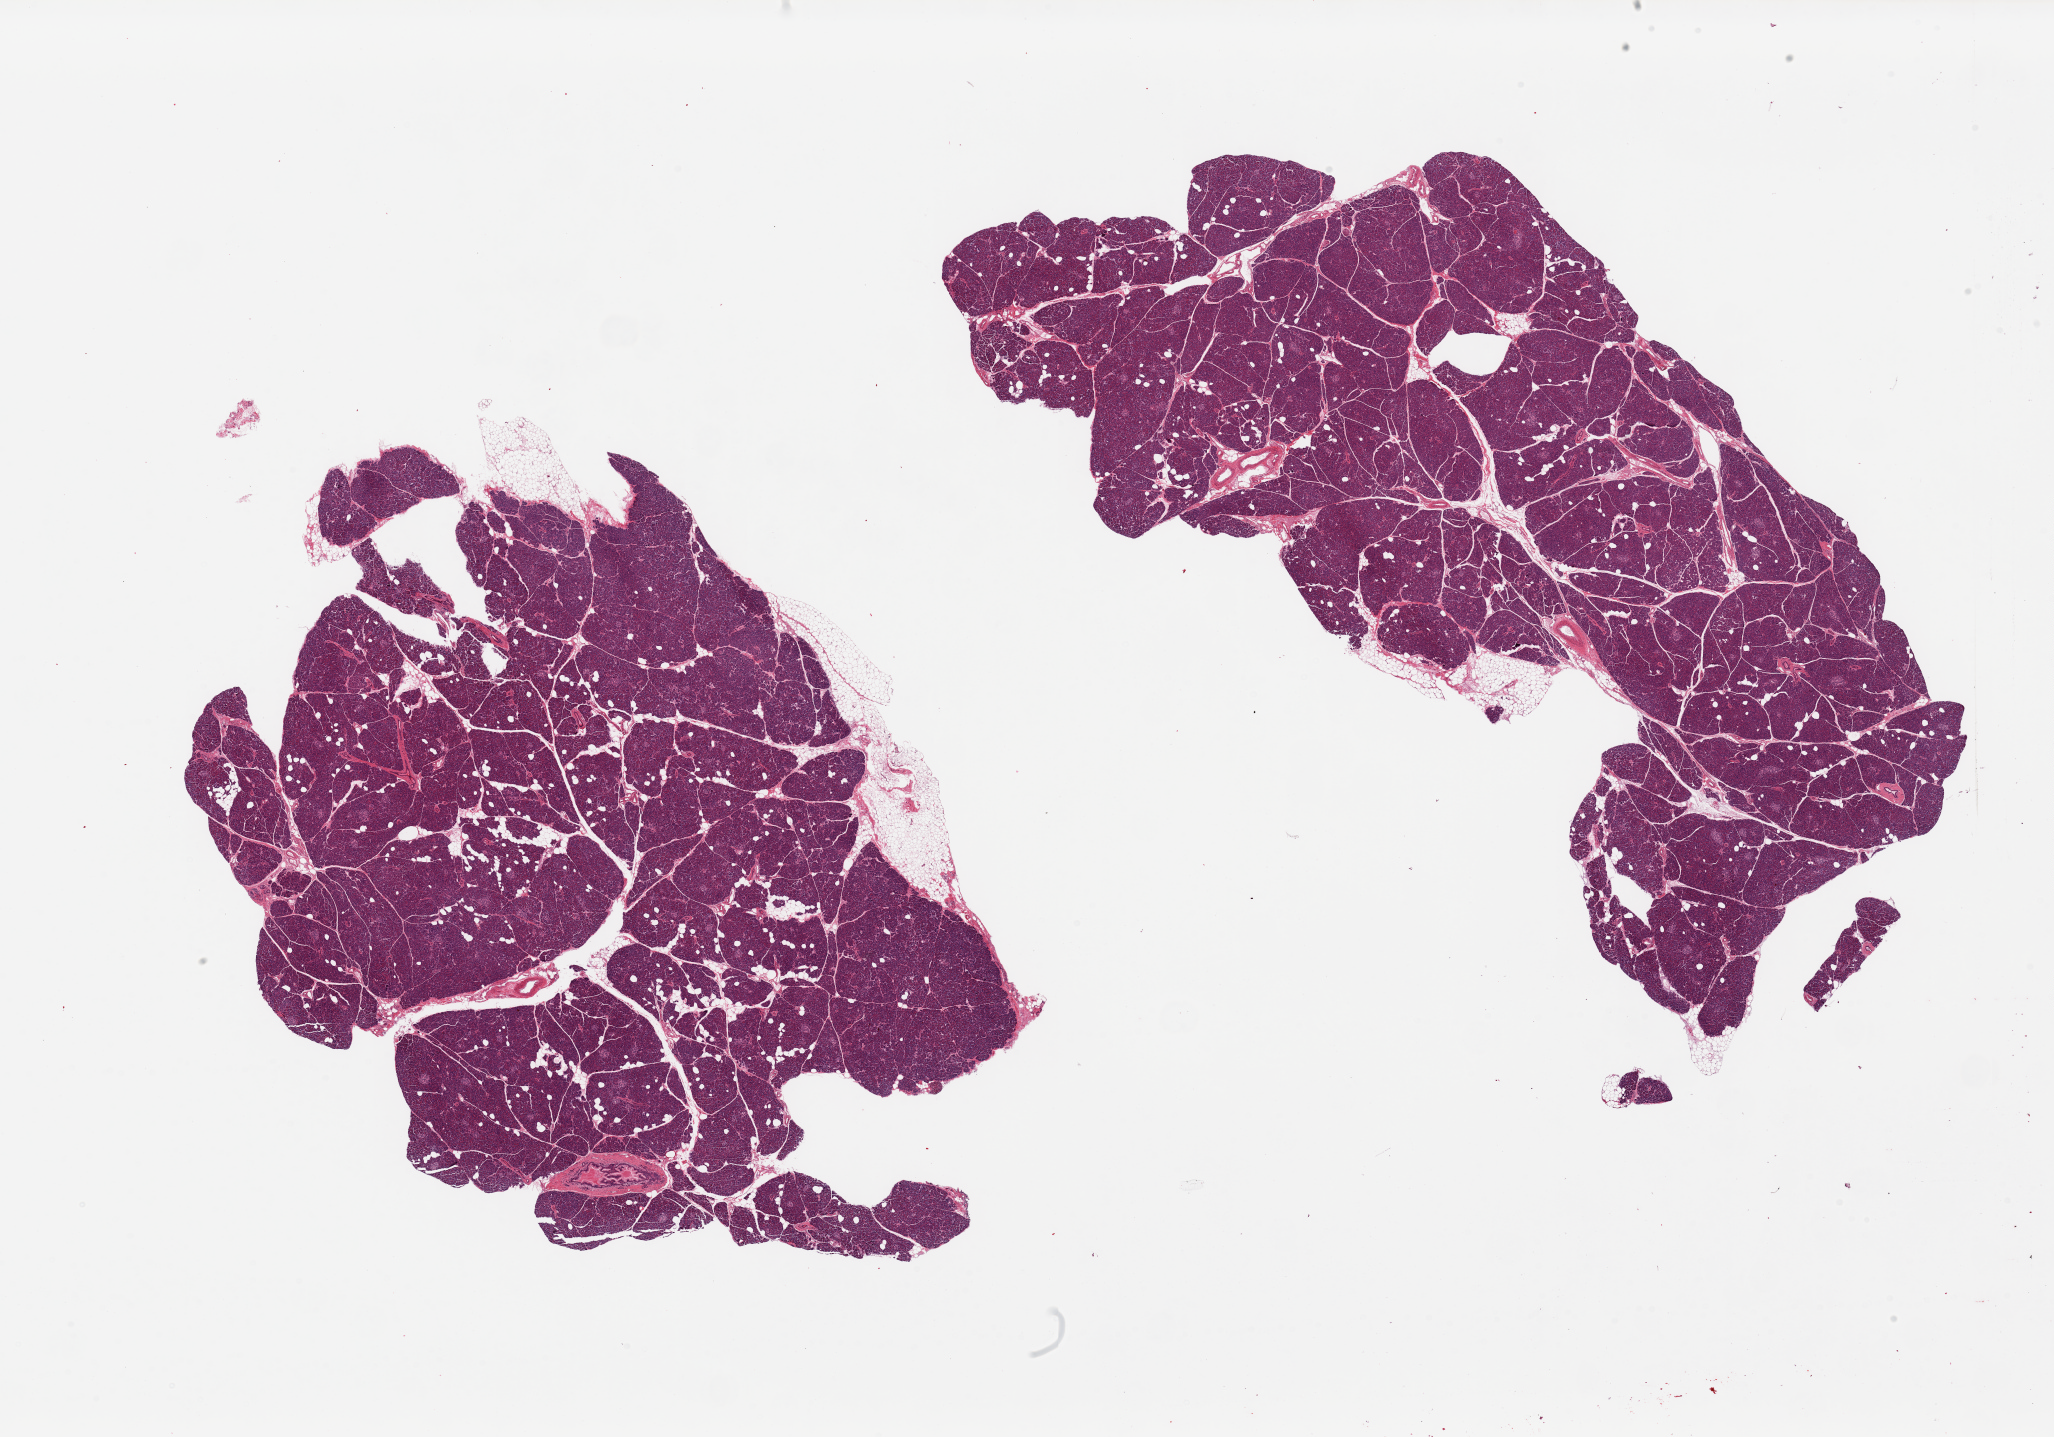
H&E whole-slide image — whole scanned area (about 32.5 x 22.7 mm) shown as a low-resolution overview. PAXgene-fixed, paraffin-embedded tissue. Section of pancreas (target tissue). Donor tissue sample. Male donor.
Pathologist's review note for this sample: 2 pieces. 5% internal fat.